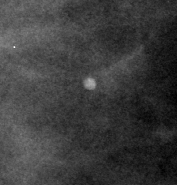
Region of interest cut from a scanned film mammogram (one marked finding), left breast, CC view.
- Calcifications, morphology punctate; BI-RADS assessment category 2; subtlety rating 3 on a 1 (subtle) to 5 (obvious) scale; benign; no additional work-up was recommended (benign without callback).